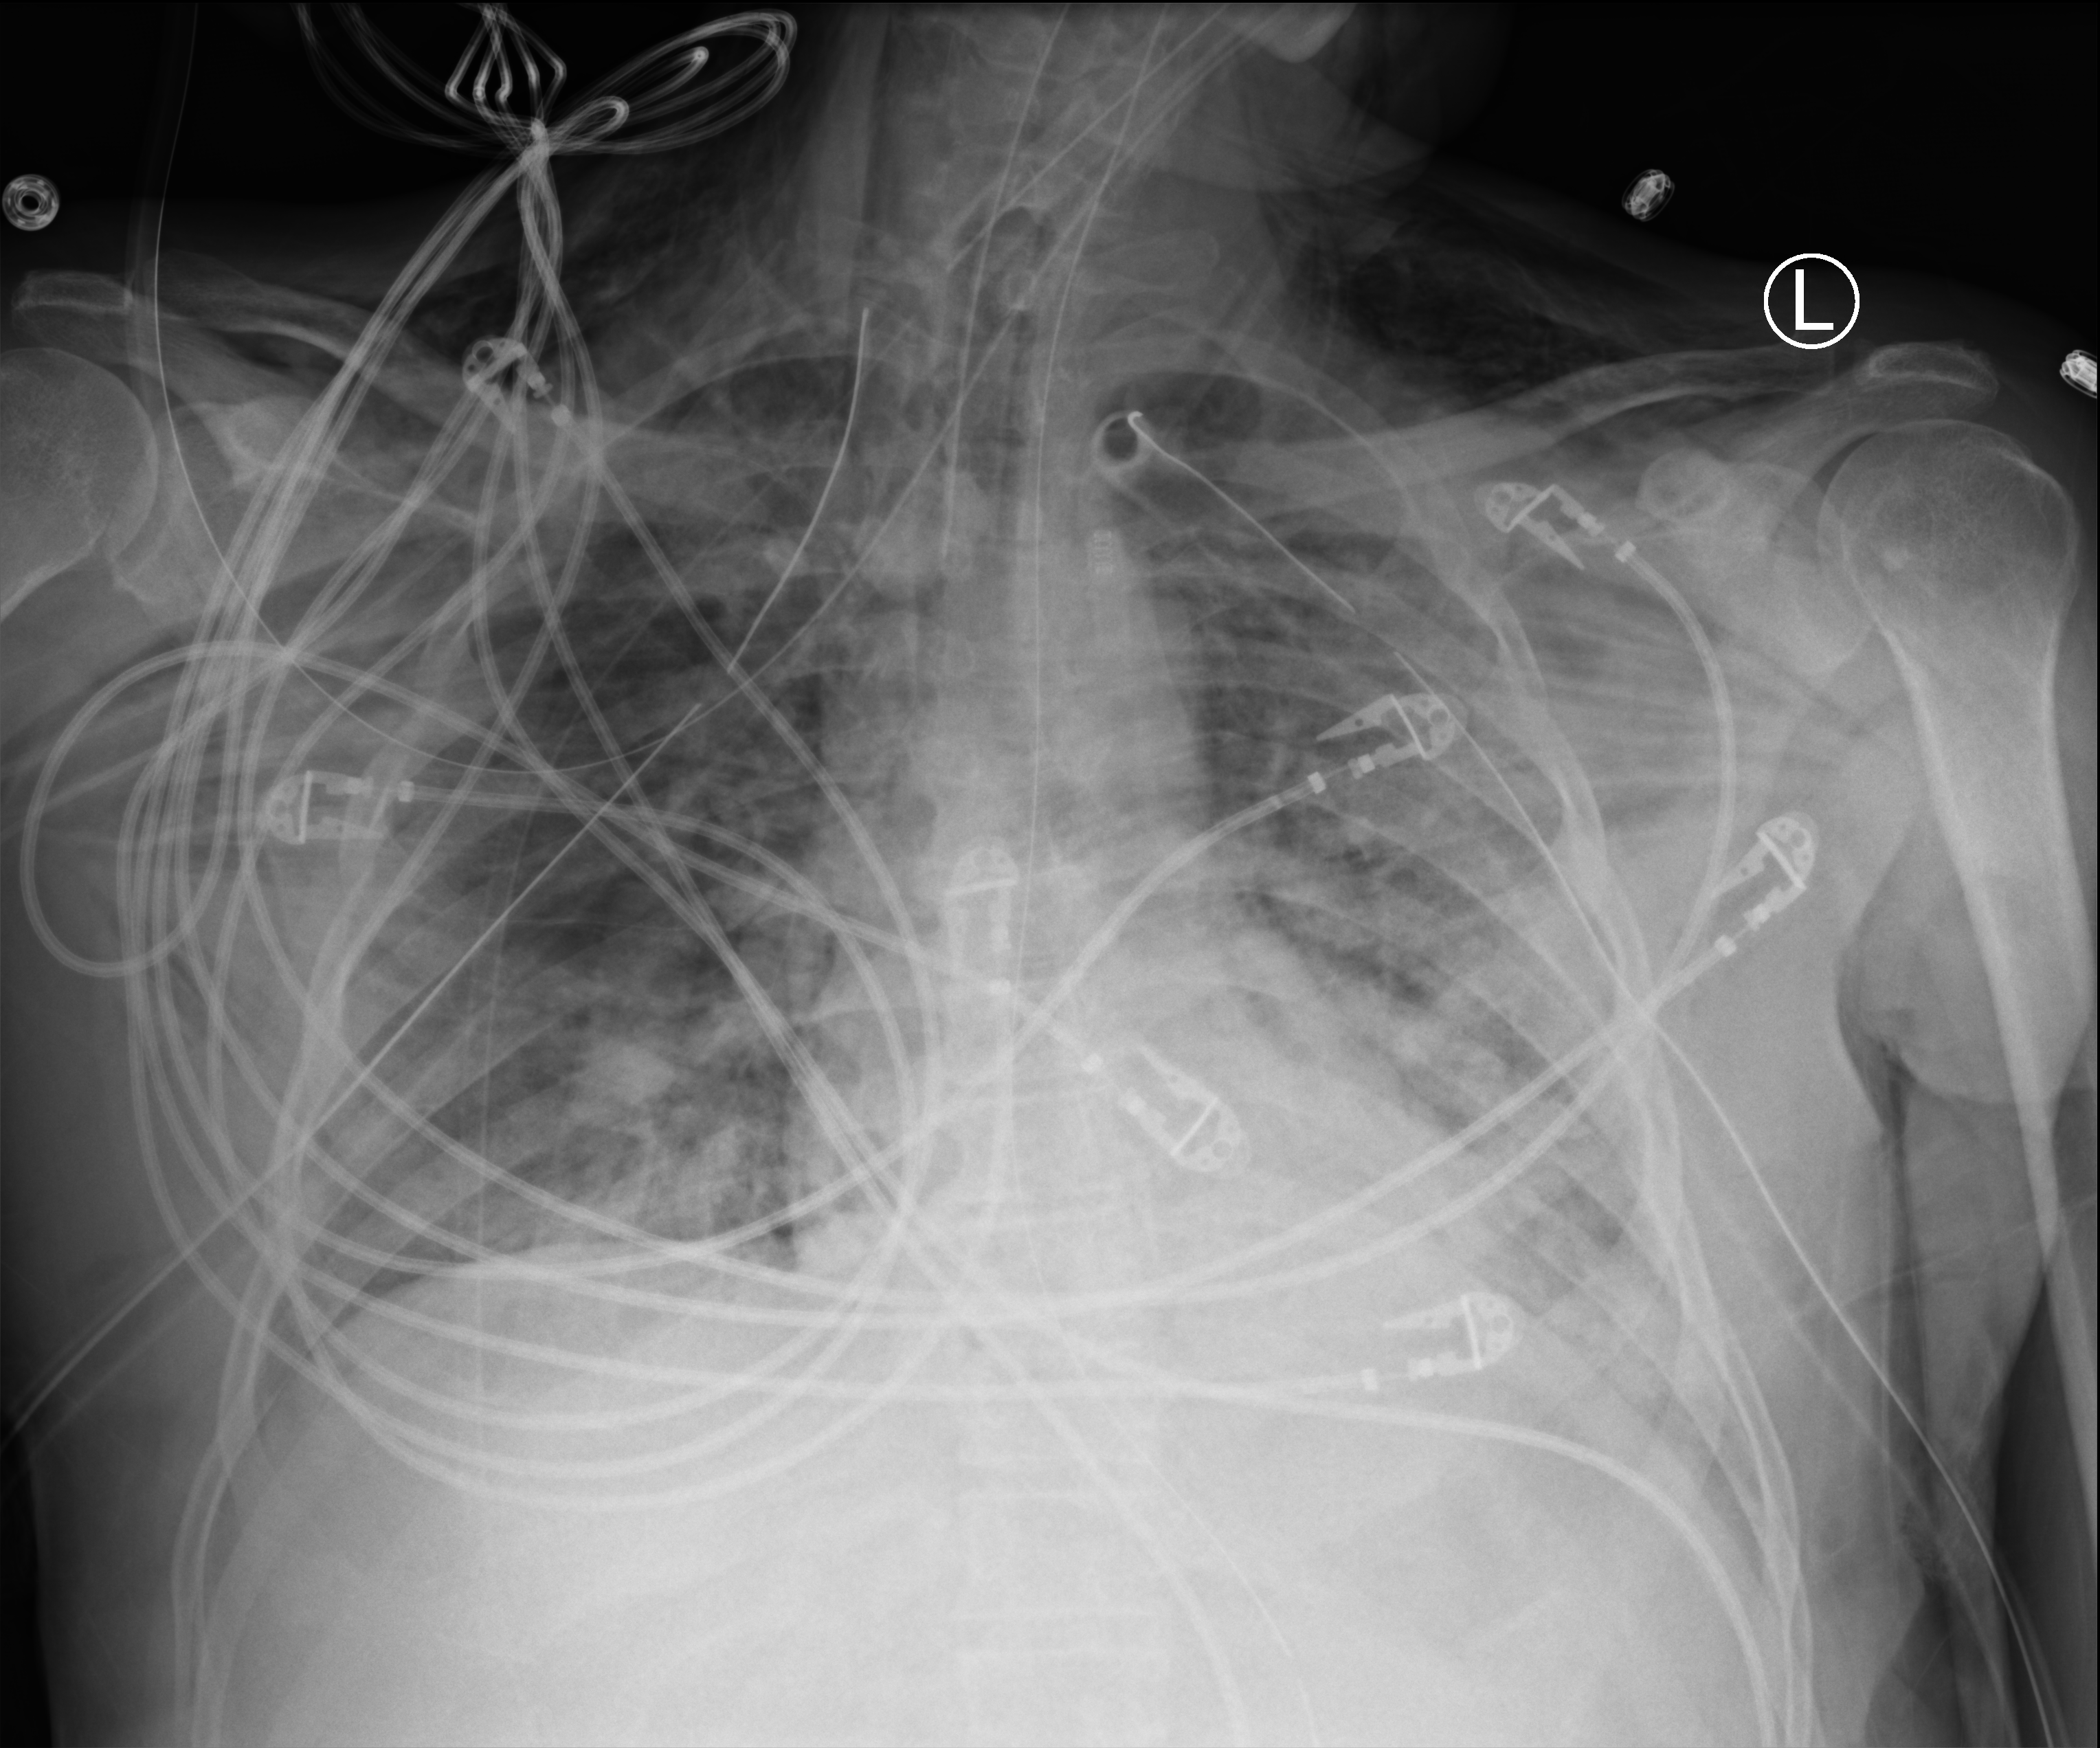
Bedside chest radiograph (computed radiography); anteroposterior (AP) projection. Patient hospitalised with COVID-19; male, aged 18–59 years.
Hospital-stay facts (about this admission, not read from this image; timing relative to this image not recorded): admitted to intensive care during this hospital stay: yes; length of hospital stay: 83 days; mechanically ventilated during this hospital stay: yes.